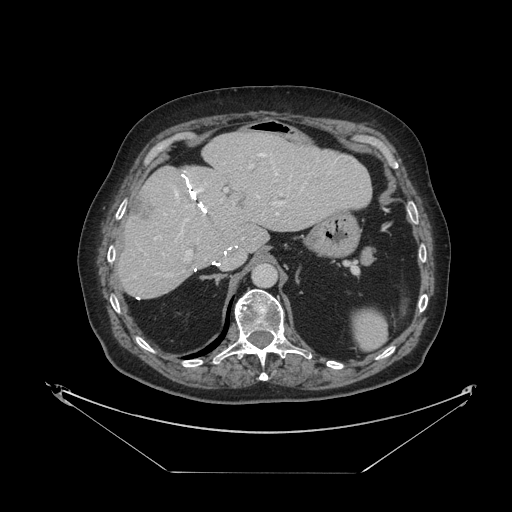
Contrast-enhanced abdominal CT, one axial slice. Position 71 of 121 along the scan axis. Reconstruction kernel STANDARD. 120 kVp. Soft-tissue window (W 400 / L 40 HU). 2.5 mm slice thickness. 512 × 512 image matrix, field of view 500 × 500 mm. Male patient, age 68 years. From the clinical record (not read from this slice): diagnosis: colorectal cancer liver metastases, imaged before liver resection; multiple liver metastases: no; largest metastasis: 4 cm; disease in both lobes: no.
Structures marked on this image (outlined manually by an expert reader):
- hepatic veins: bounding box (x1, y1, x2, y2) in pixels: (155, 153, 282, 239)
- liver: (119, 131, 371, 299)
- planned liver remnant (the part of the liver to remain after resection): (119, 131, 371, 299)
- portal vein (with intrahepatic branches): (165, 165, 282, 277)
- liver metastasis: (132, 196, 155, 223)